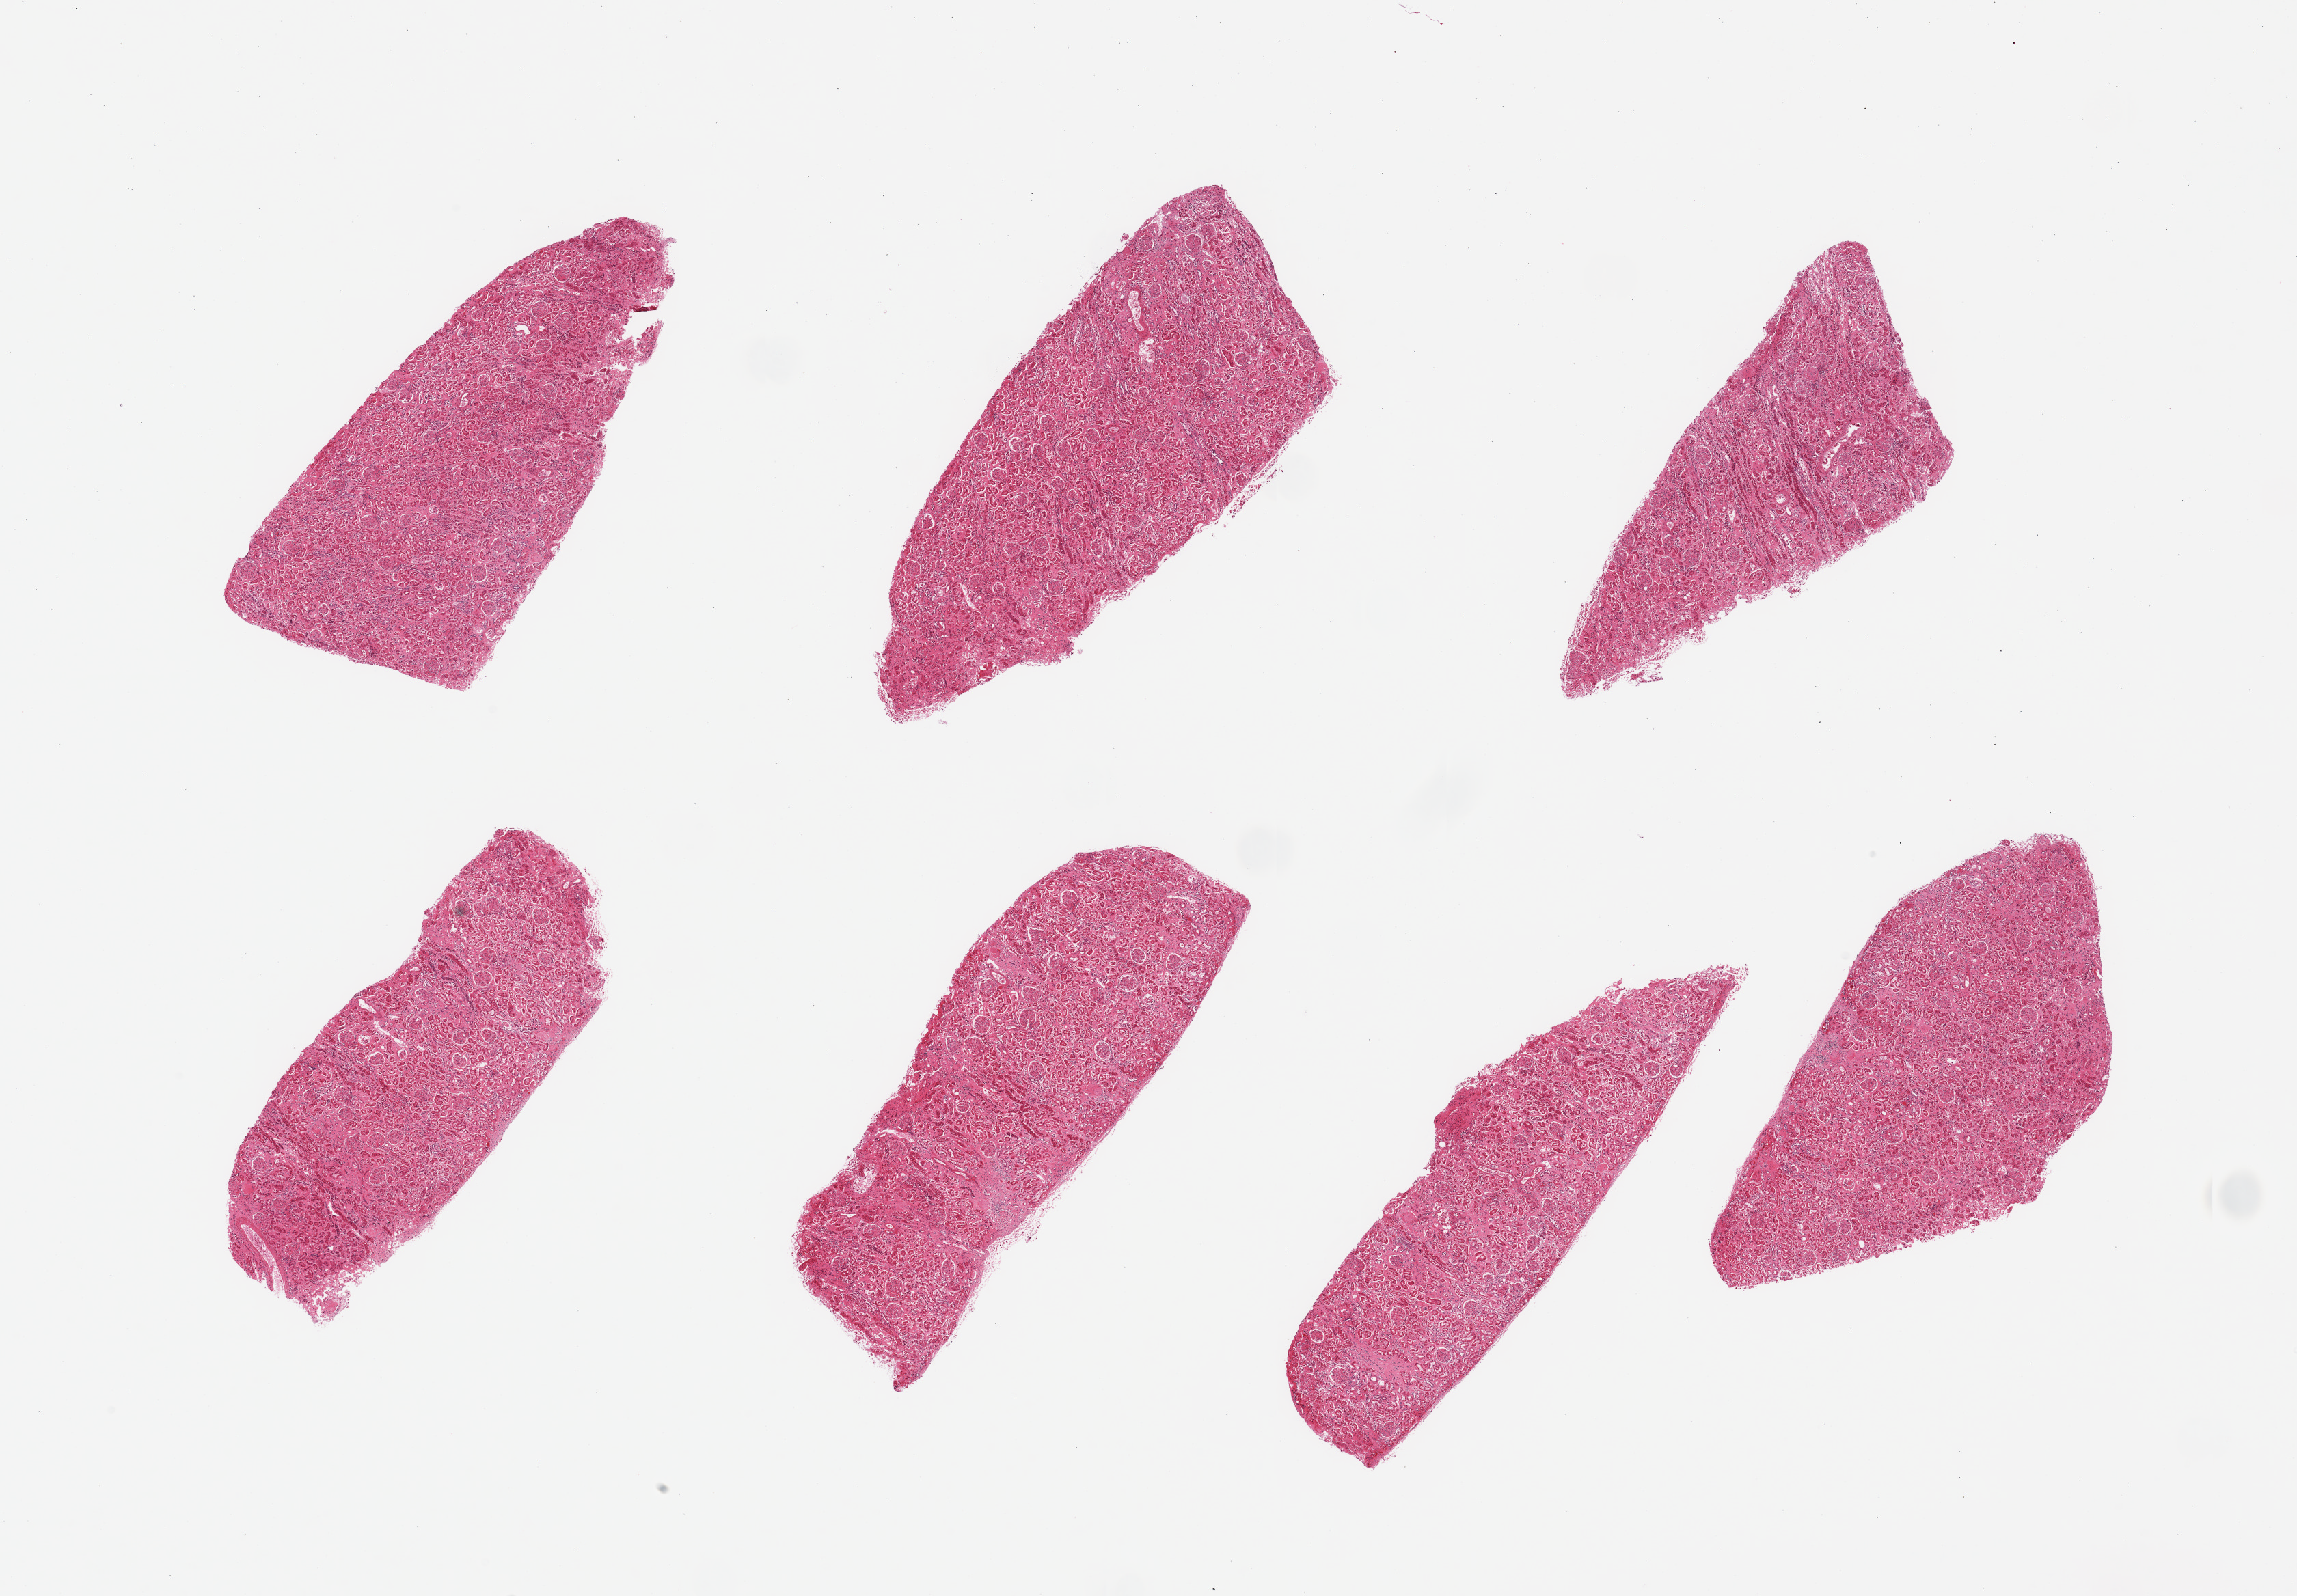
Haematoxylin and eosin whole-slide image, whole scanned area (about 26.6 x 18.5 mm) shown as a low-resolution overview; PAXgene-fixed, paraffin-embedded tissue; section of renal cortex (target tissue); tissue donor sample.
Pathologist's review note for this sample: 7 pieces; moderate to marked degree of diffuse glomerular sclerosis.